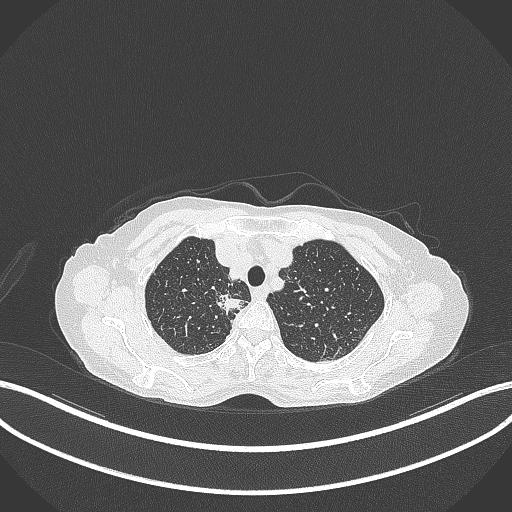
Chest CT, one axial slice. Position 309 of 403 along the scan axis. Reconstruction kernel B70f. 120 kVp. Lung window (W 1500 / L -600 HU). 512 × 512 image matrix. Patient: female, 75 years. Case-level facts recorded for this patient, not image findings: clinical TNM (as recorded): T1c N1 M1.
Annotated regions visible in this slice (rectangle marked by the reading radiologist):
- lung tumour (recorded histology: adenocarcinoma): box from (x=216, y=293) to (x=245, y=313) px